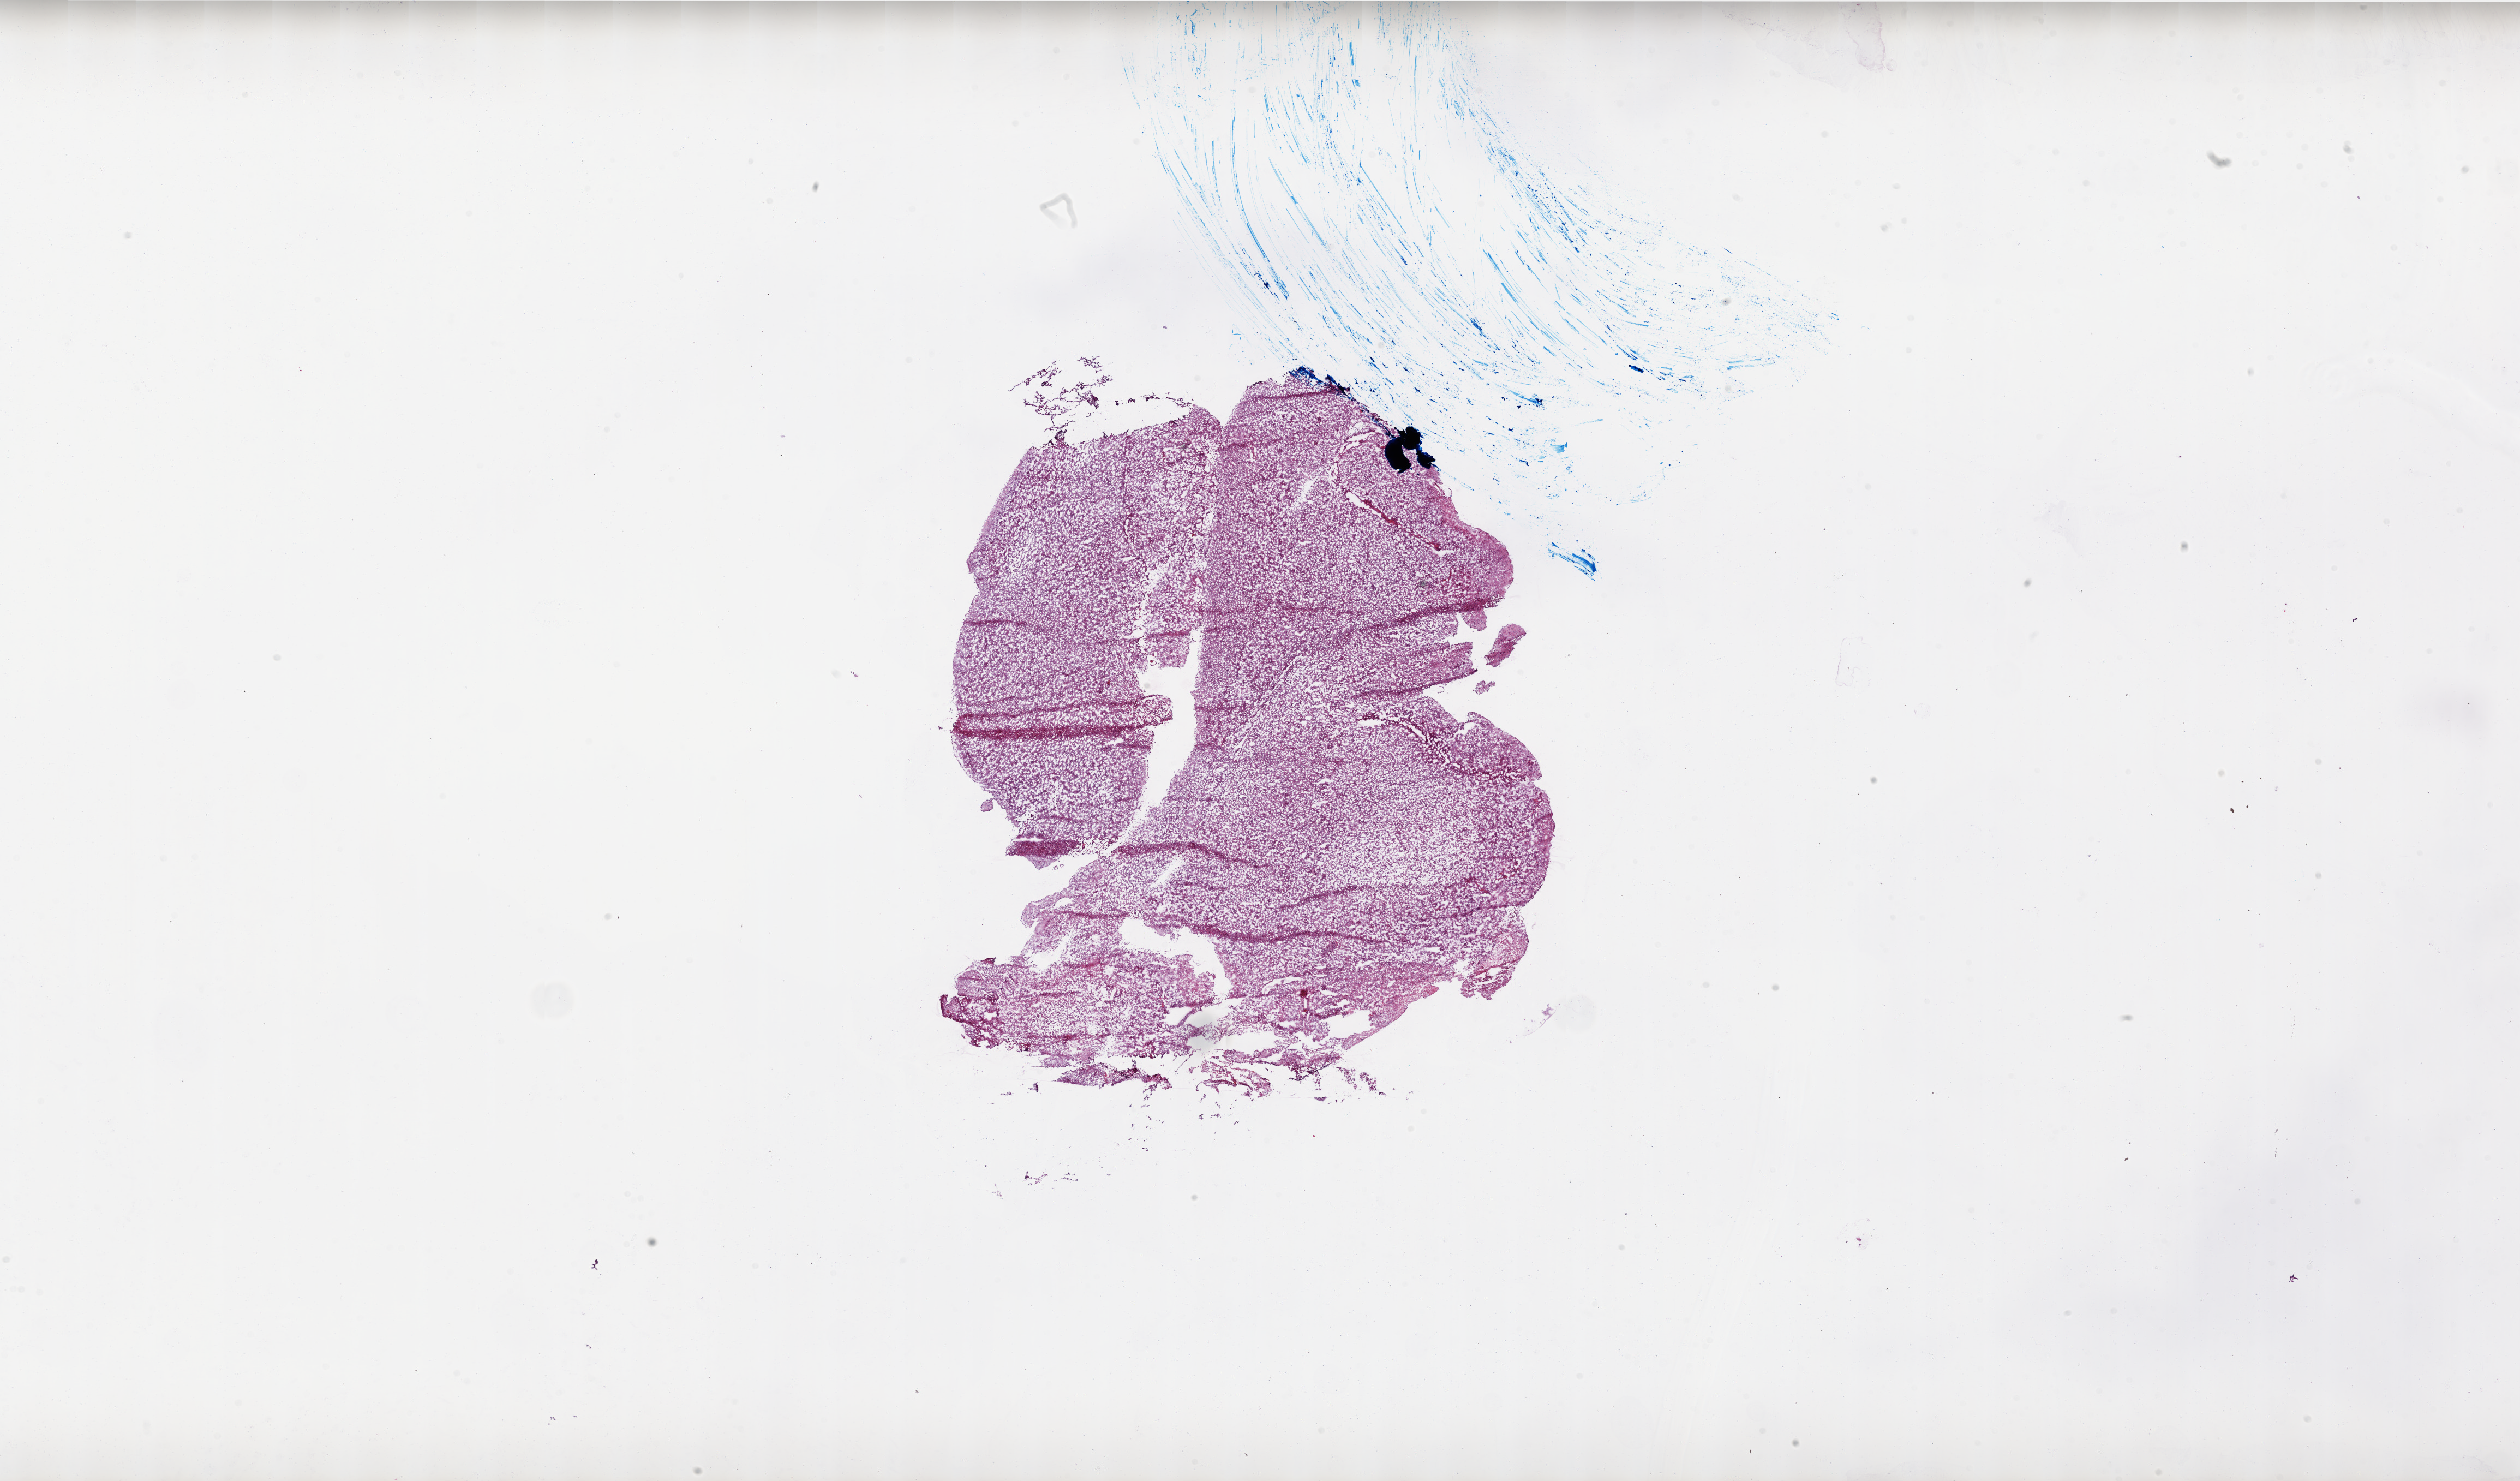
Whole-slide histology image, H&E-stained — low-resolution overview of the scanned area, about 37.0 x 21.7 mm, frozen section from the top of the tissue portion, primary tumour sample from the brain. Female, age 69 years at initial diagnosis. Composition of this section per pathologist review: tumour cells 90%, tumour nuclei 95%, normal cells 0%, stromal cells 10%, necrosis 0%.
Histologic diagnosis: Glioblastoma.